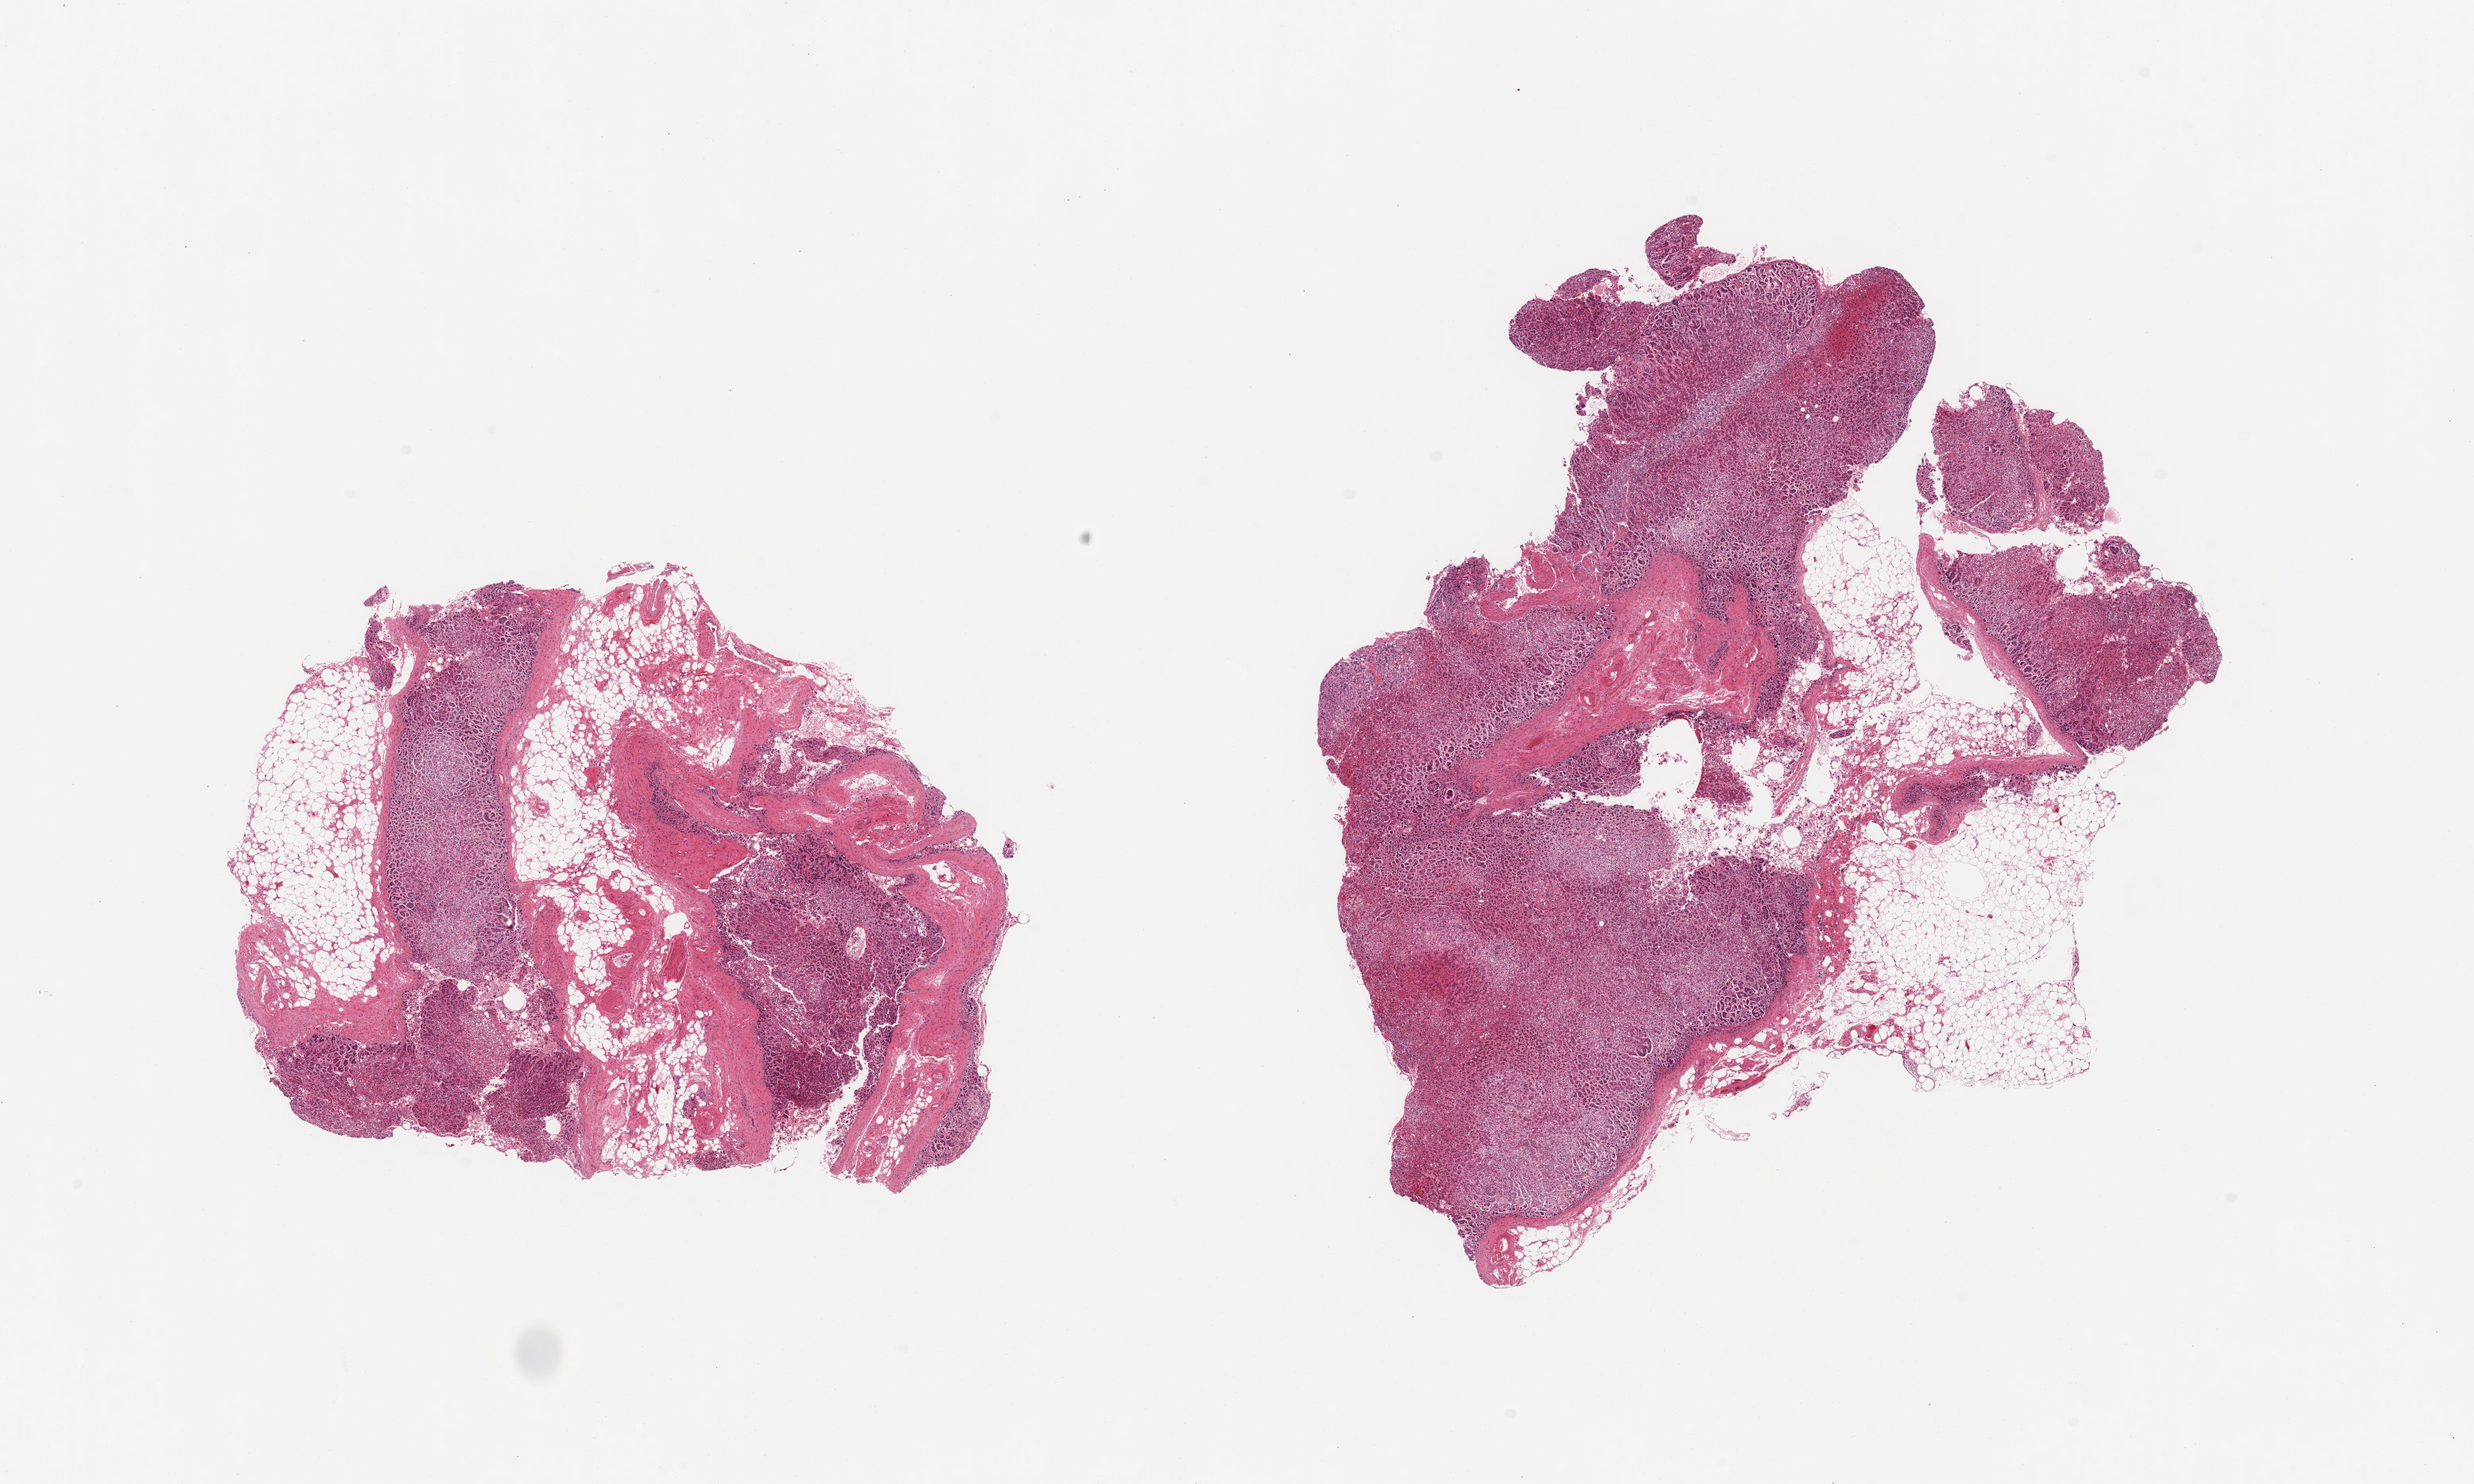
Whole-slide image, haematoxylin and eosin stain, shown as a low-resolution overview of the whole scanned area (about 24.6 x 14.8 mm); PAXgene-fixed, paraffin-embedded tissue; target tissue: adrenal gland; donor tissue sample.
* reviewer comment on this tissue sample: 2 pieces; 30 & 50% internal fat & vascular content